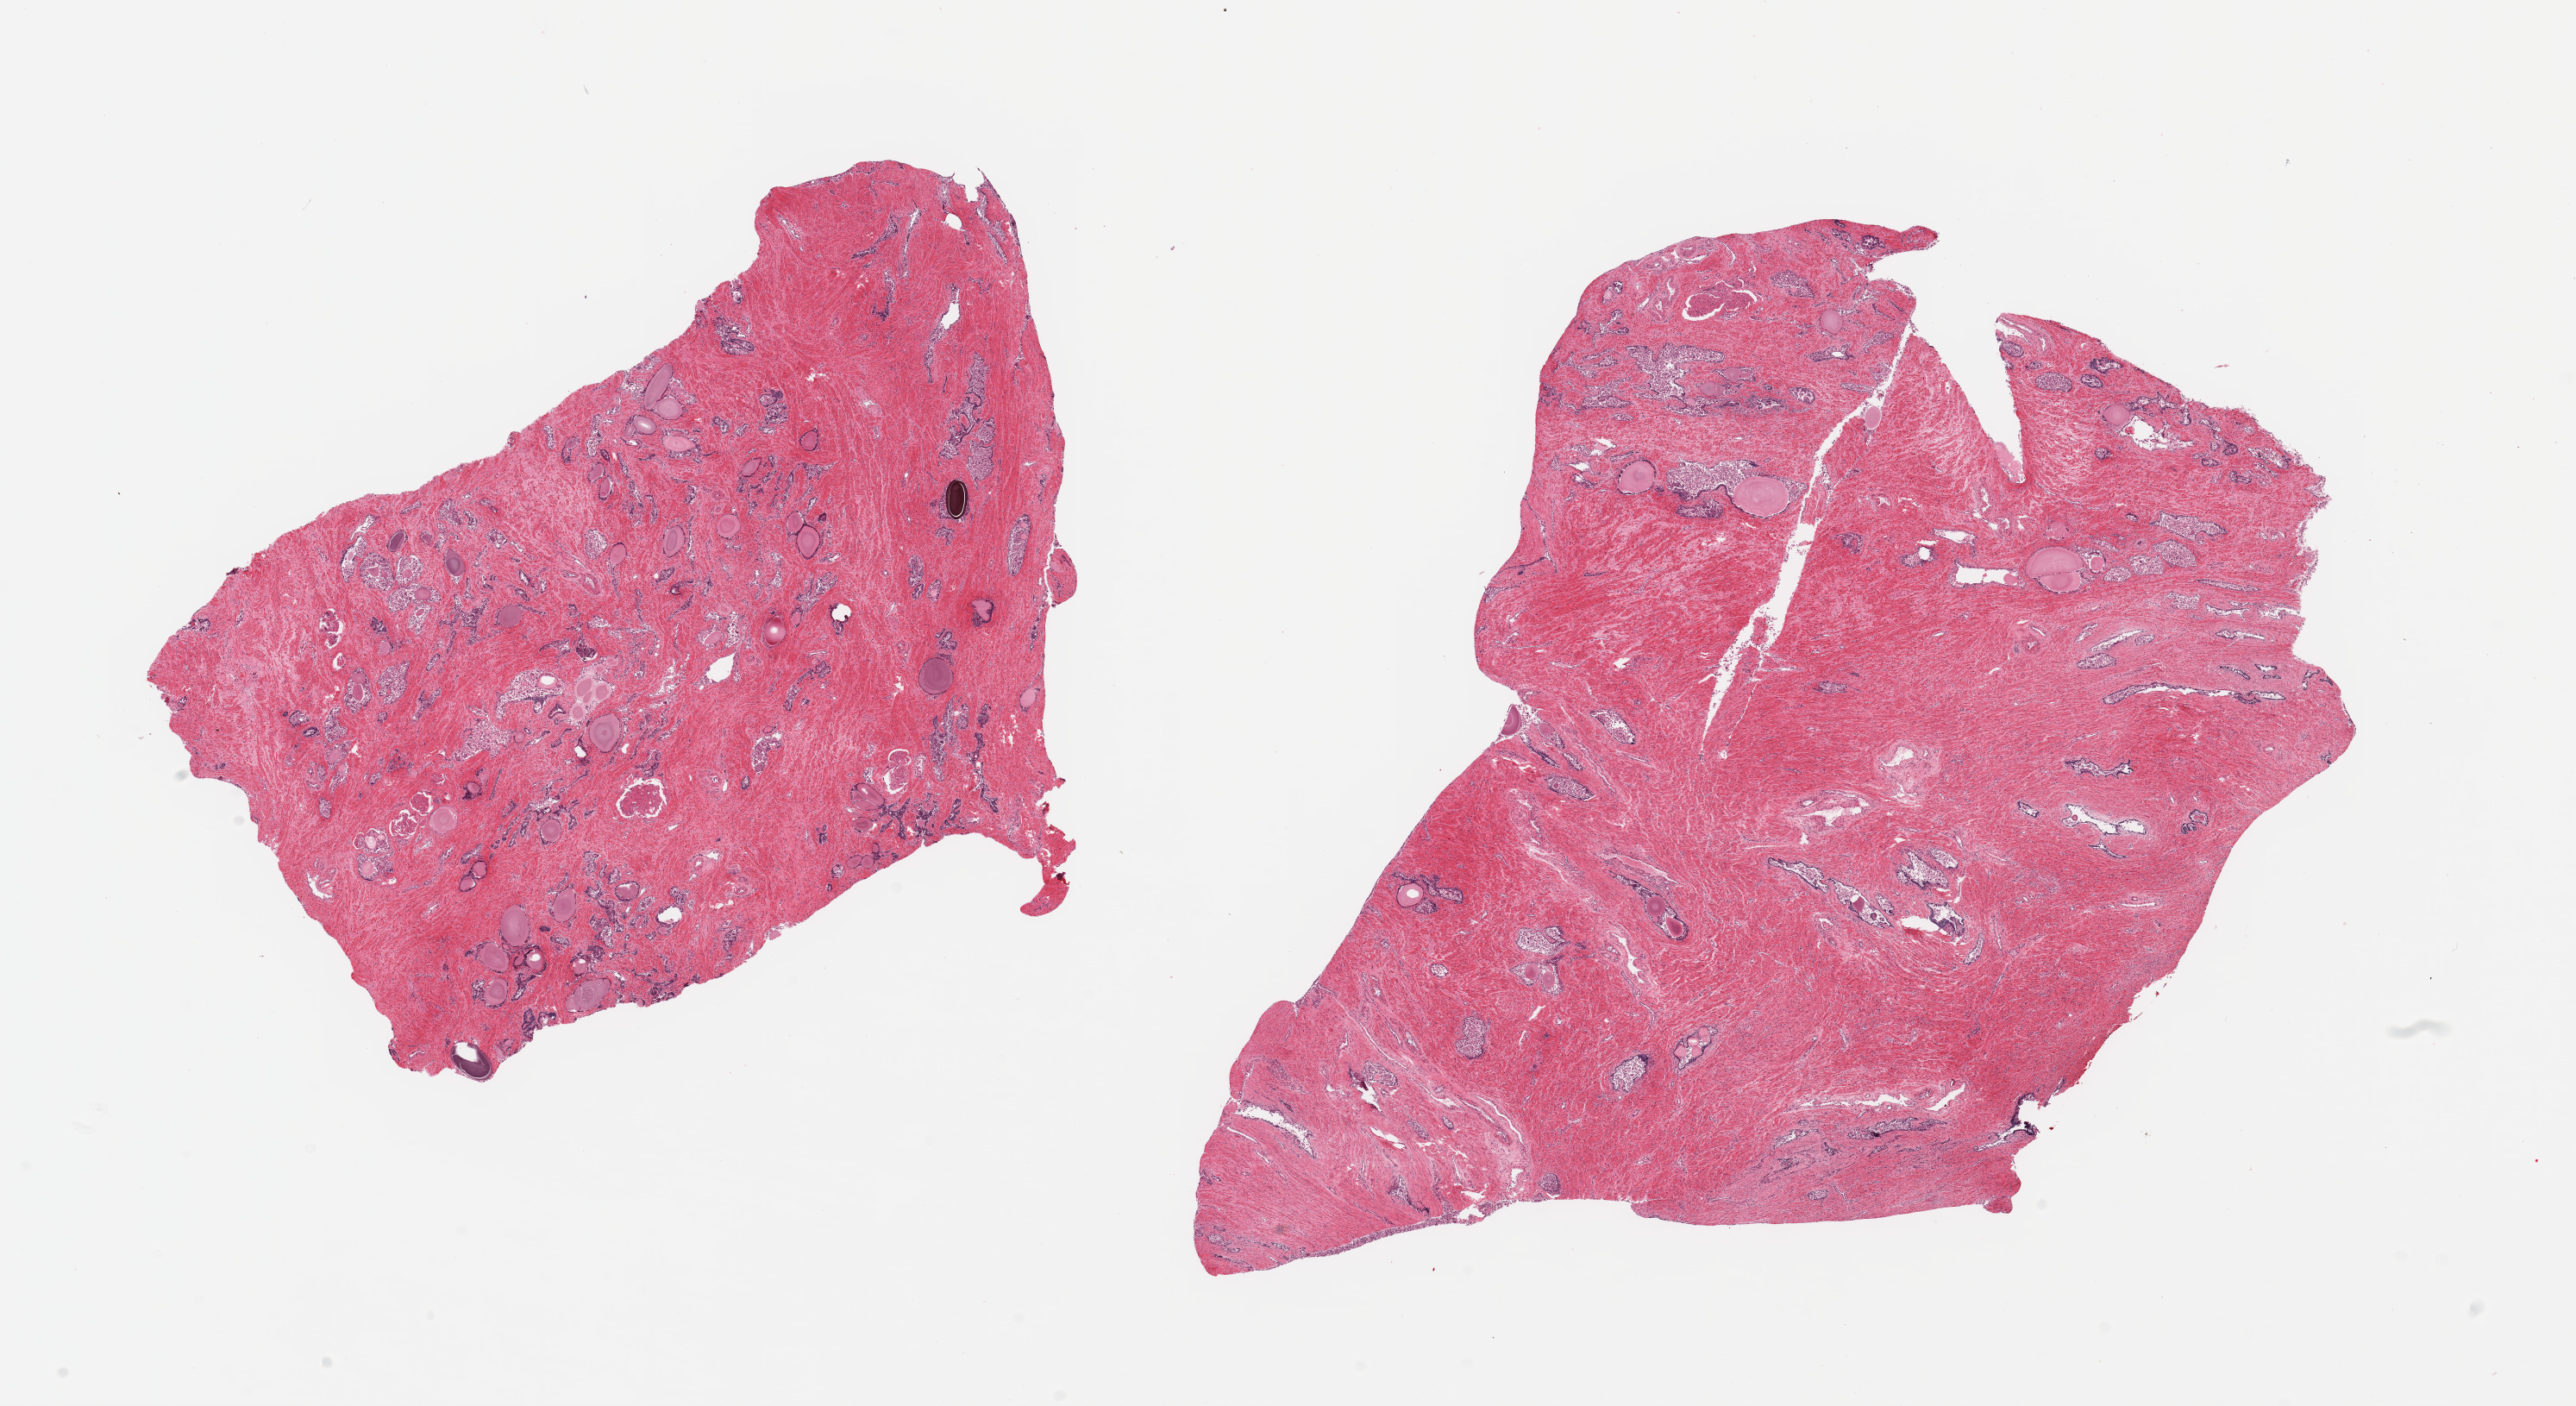
H&E whole-slide image, a low-resolution overview of the entire scanned area, about 23.6 x 12.9 mm (from a 20x scan); PAXgene-fixed, paraffin-embedded tissue; section of prostate (target tissue); donor tissue sample. Donor: male.
- review note (as recorded): 2 pieces, glandular elements with autolysis ranging from score 1 to score 3